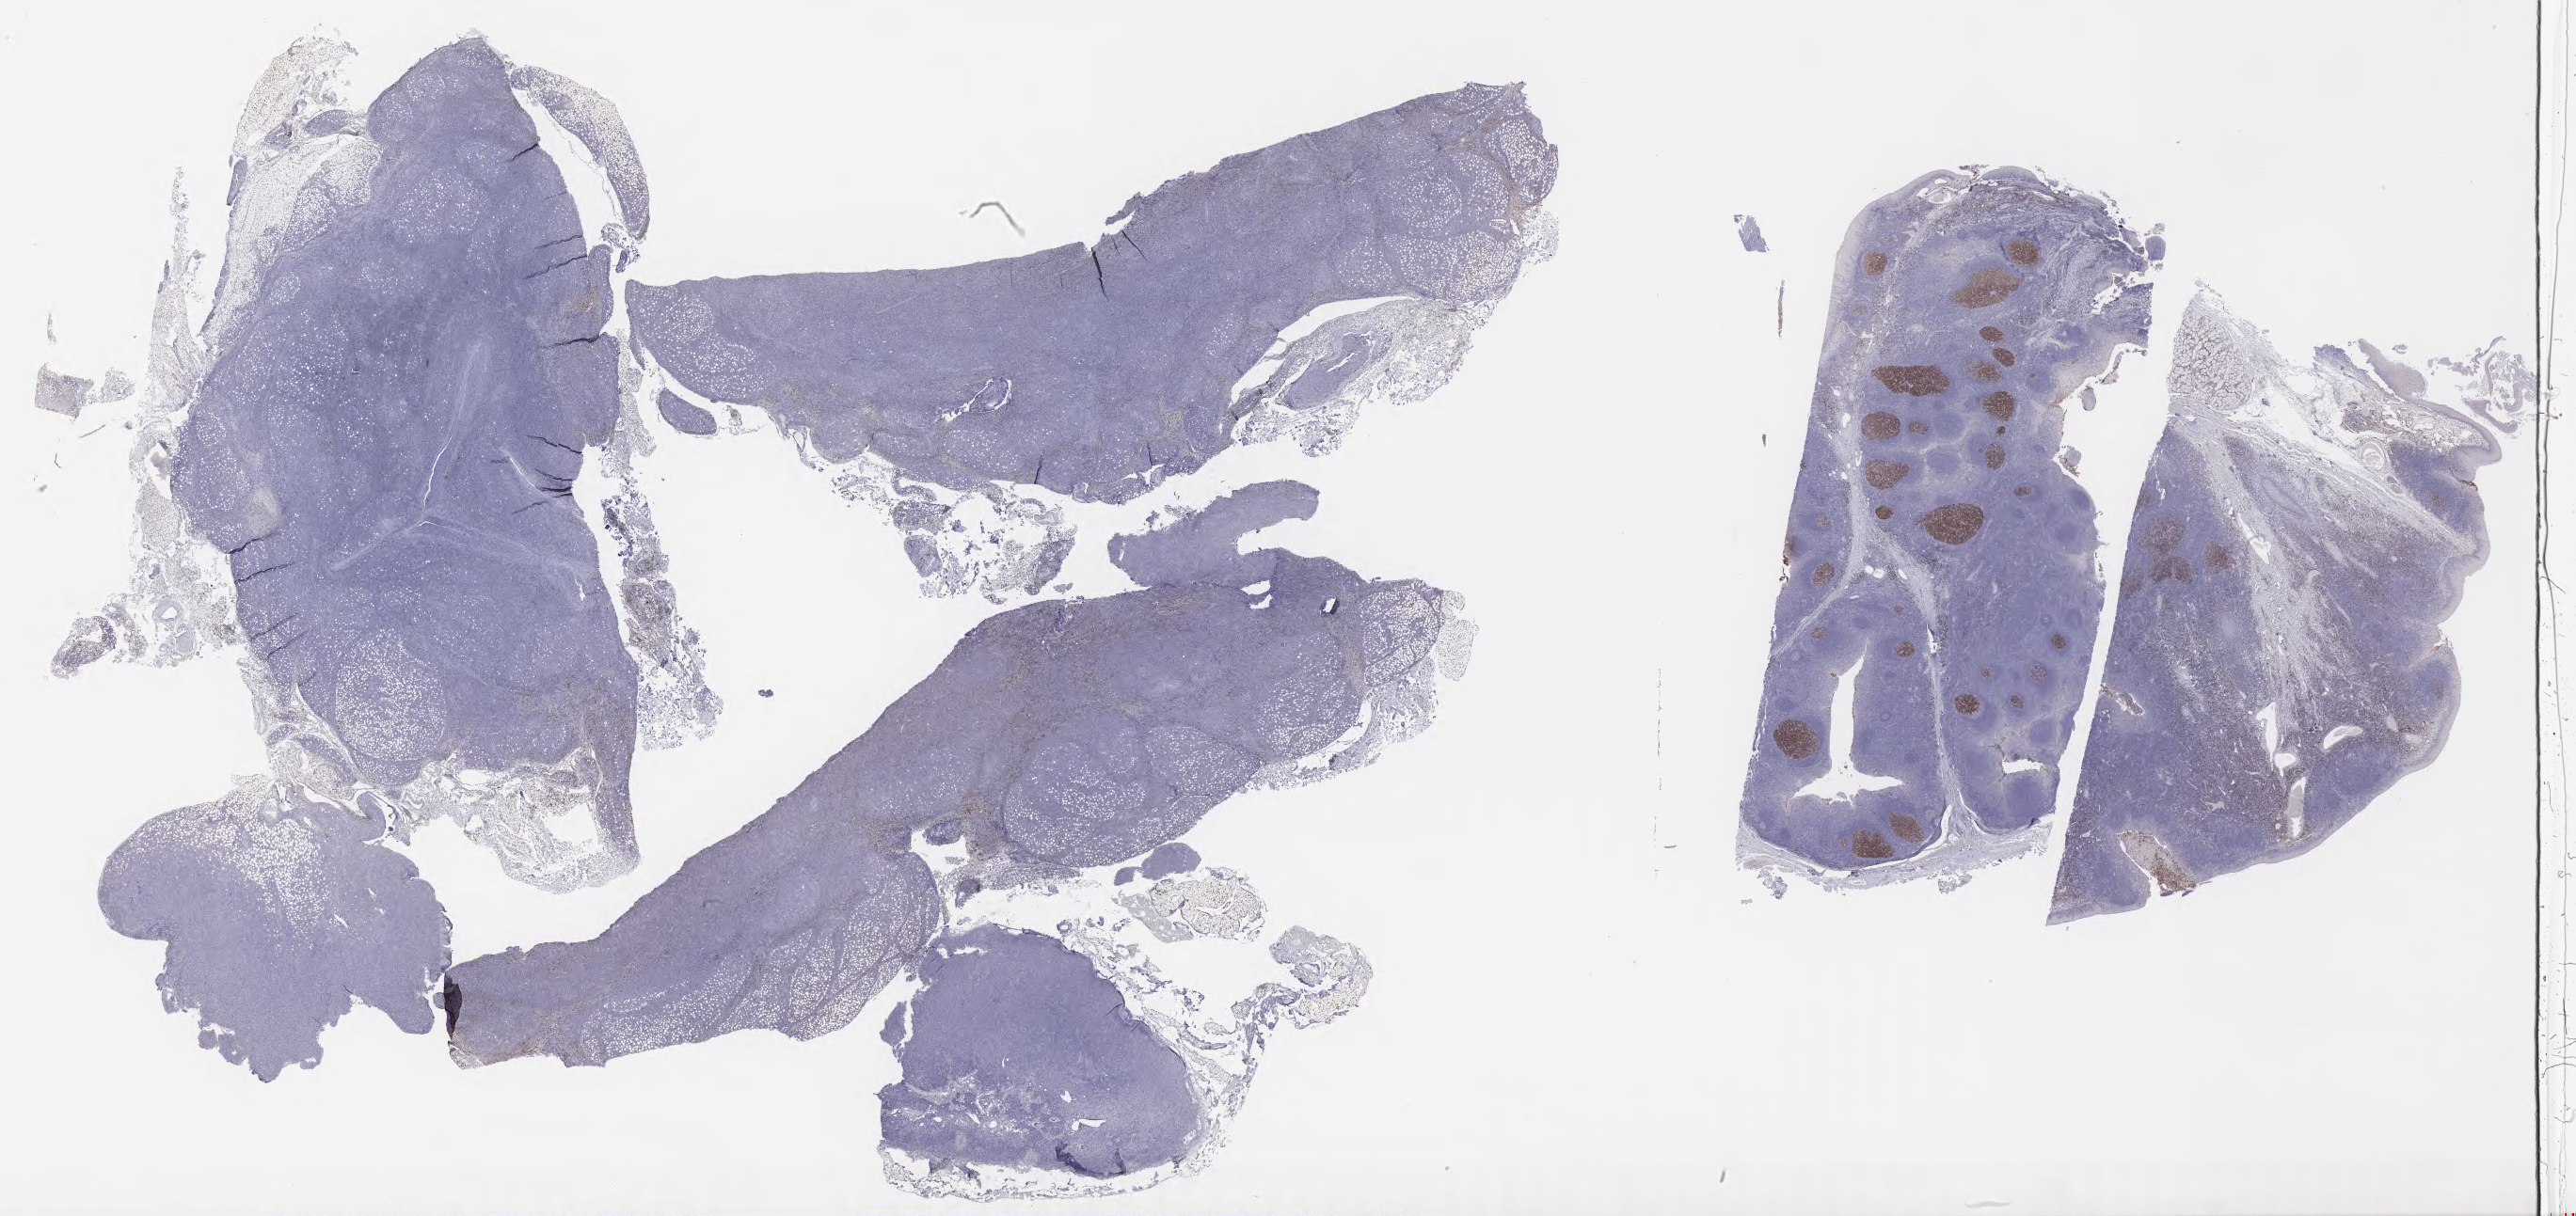
IHC for CD10, whole-slide image, whole scanned area (about 44.3 x 20.9 mm) shown as a low-resolution overview. Specimen: tumor tissue. Anatomic site: lymph node. Male patient, aged 68.
* diagnosis: Diffuse large B-cell lymphoma, NOS